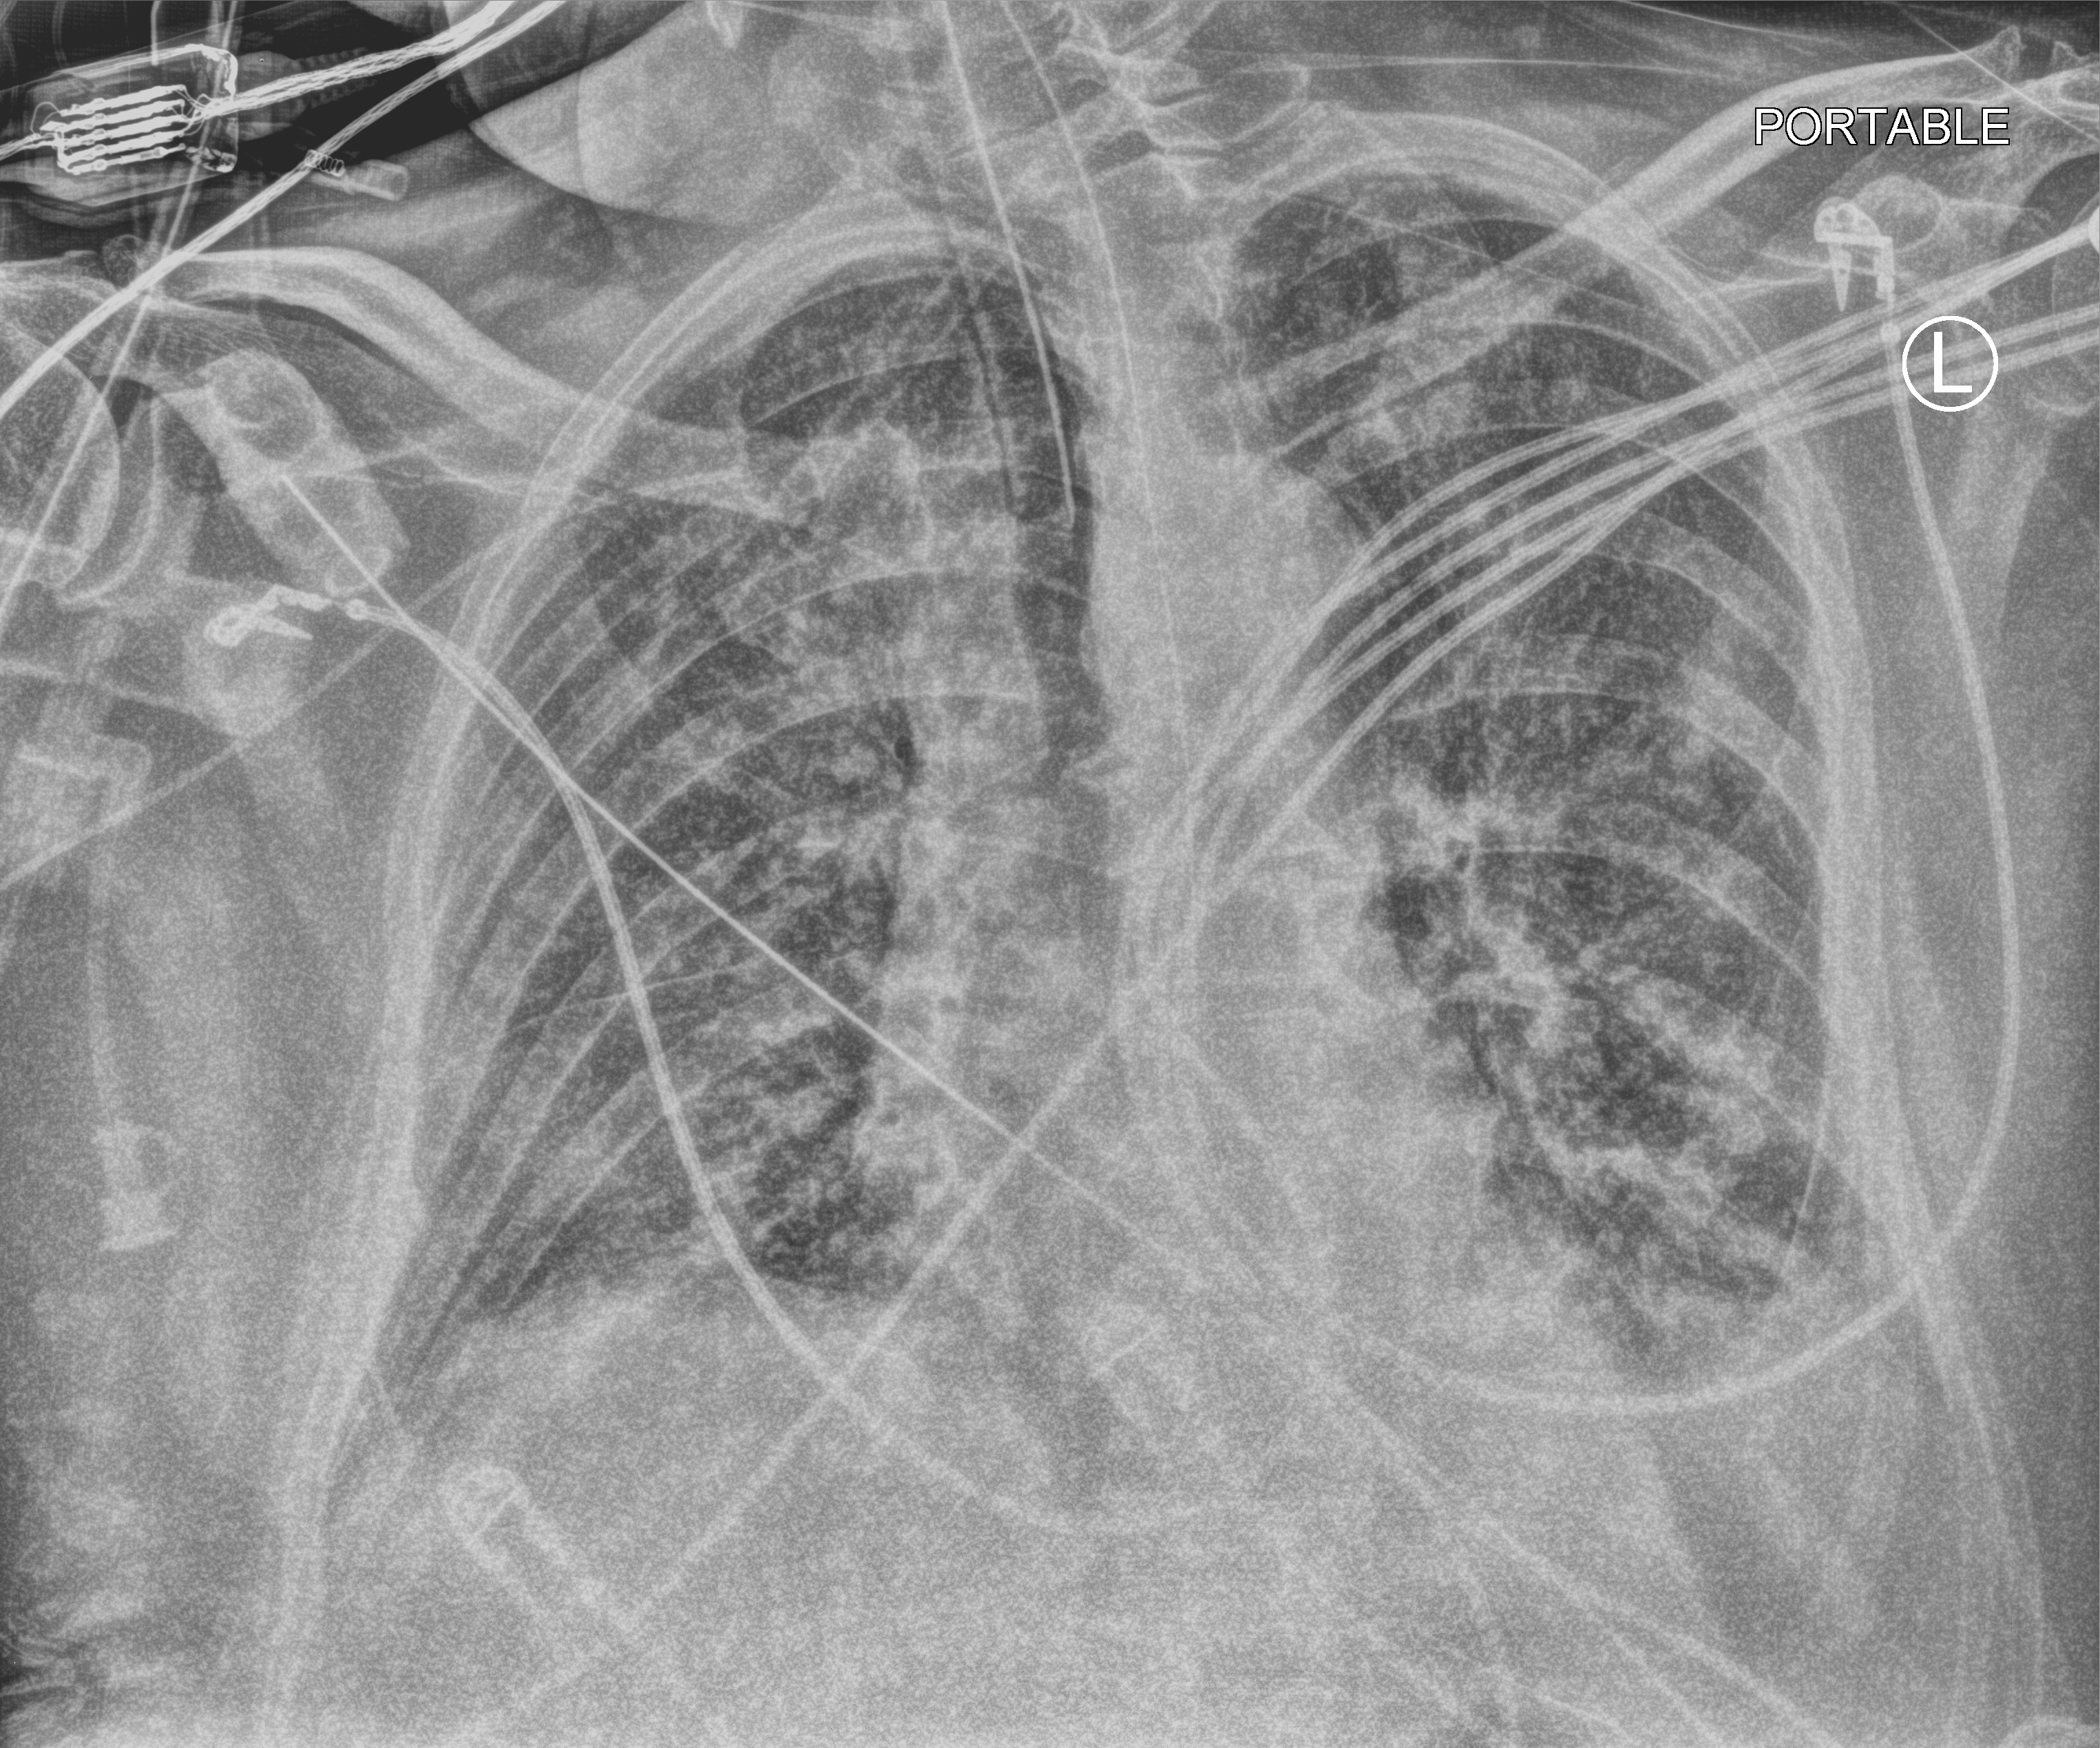
Portable chest radiograph; anteroposterior (AP) projection. Male patient hospitalised with COVID-19, age 60–74 years.
Hospital-stay facts (about this admission, not read from this image; timing relative to this image not recorded):
- admitted to intensive care during this hospital stay: yes
- length of hospital stay: 20 days
- mechanically ventilated during this hospital stay: yes